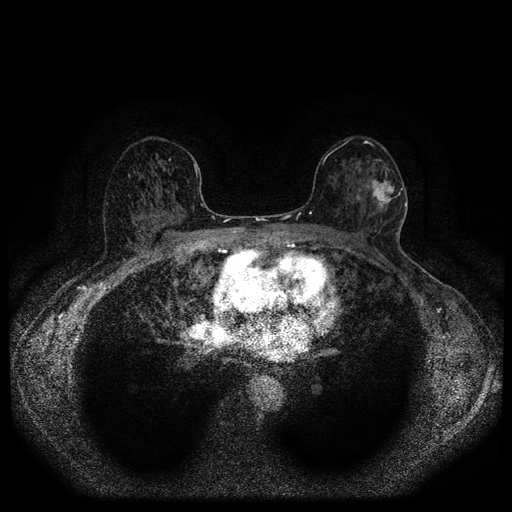
Breast MRI (dynamic contrast-enhanced, multi-phase), one axial slice; position 59 of 116 along the scan axis; dynamic contrast-enhanced series, time point 2 of 5 at this slice position (early post-contrast); 1.5 T; TE 2.7 ms, TR 5.4 ms; 2 mm slice thickness; 512 × 512 image matrix, field of view 330 × 330 mm. Patient: female, 56 years.
Outlined on this slice (semi-automatic segmentation, software-assisted and operator-edited):
- breast lesion (labelled 'tumour' in the annotation; benign lesions carry a separate 'benign' label): bounding box <366,163,403,209> (left, top, right, bottom; pixels)